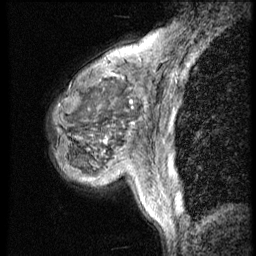
Breast MRI (dynamic contrast-enhanced), one sagittal slice; slice 14 of 56 in the series (ordered by position); 4 images stored at this slice position (order not interpretable as contrast timing); 1.5 T; TE 4.2 ms, TR 9 ms; 2.5 mm slice thickness; 256 × 256 image matrix. Female patient, age 50 years. From the clinical record (not read from this slice): setting: breast cancer imaged before/during neoadjuvant chemotherapy; receptor status: triple-negative.
Annotated regions visible in this slice (semi-automatic segmentation, software-assisted and operator-edited):
- analysis volume of interest (the breast-tissue region the enhancement analysis was run in; not a lesion): bounding box (x1, y1, x2, y2) in pixels: (46, 46, 148, 188)
- tumour enhancement mask (voxels above the 140 % enhancement threshold inside the analysis volume of interest): (104, 48, 139, 143)